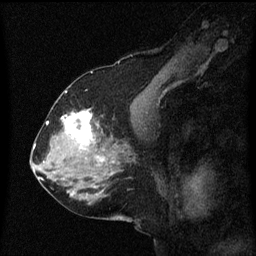
Breast MRI (dynamic contrast-enhanced), one sagittal slice. Dynamic contrast-enhanced series, image 2 of 3 at this slice position (ordered by acquisition). 1.5 T. TE 4.2 ms, TR 8.4 ms. 256 × 256 image matrix. Female patient, age 58 years.
Annotated regions visible in this slice (semi-automatic segmentation, software-assisted and operator-edited):
- analysis volume of interest (the breast-tissue region the enhancement analysis was run in; not a lesion): box from (x=58, y=110) to (x=99, y=151) px
- tumour enhancement mask (voxels above the 70 % enhancement threshold inside the analysis volume of interest): (x=64, y=110)–(x=97, y=145)